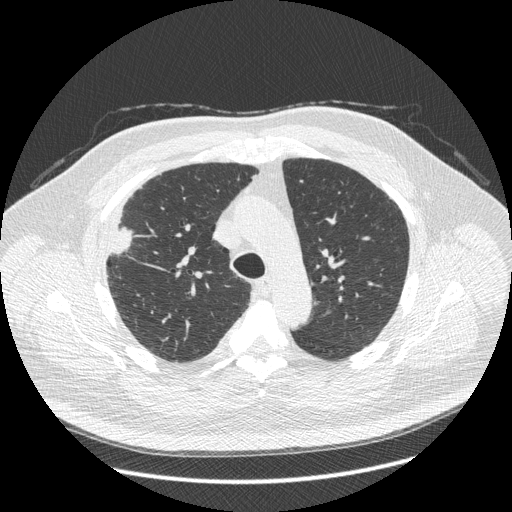
Chest CT (low-dose screening protocol), one axial image. Third screening round (two years after baseline). Lung window (W 1500 / L -600 HU). 1.25 mm slice thickness. 512 × 512 image matrix, field of view 400 × 400 mm. Male participant, aged 66 years at enrolment.
Lesion marked by an expert reader, bounding box <88,207,148,270> (left, top, right, bottom; pixels). Reader record for this screening exam (exam-level; its link to the box is not recorded): non-calcified nodule or mass ≥4 mm, right upper lobe, 48 × 25 mm, spiculated (stellate) margins, soft tissue attenuation, pre-existing on the prior screen: no. Lung cancer was diagnosed 35 days after this screen: non-small cell carcinoma, right upper lobe, stage IV (AJCC 6th edition), 50 mm at pathology.